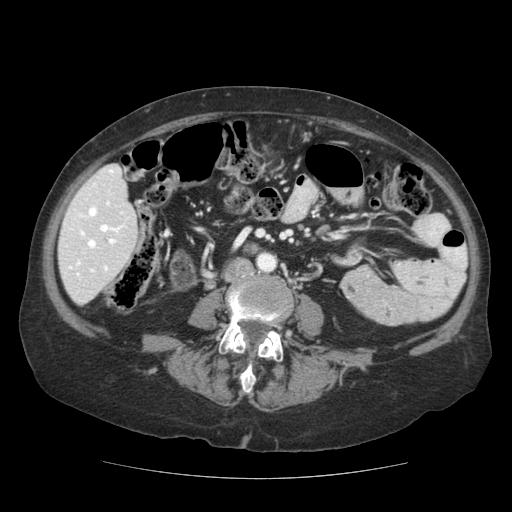
Contrast-enhanced abdominal CT (liver protocol), one axial slice. Position 37 of 111 along the scan axis. Reconstruction kernel STANDARD. 140 kVp. Soft-tissue window (W 400 / L 40 HU). 512 × 512 image matrix, field of view 360 × 360 mm. From the clinical record (not read from this slice): diagnosis: hepatocellular carcinoma (patient treated with transarterial chemoembolisation; whether this scan precedes or follows treatment is not stated here); TNM stage (as recorded): Stage-I; Child-Pugh class: A; tumour differentiation: moderately-poorly differentiated; tumour nodularity: uninodular.
Structures marked on this image (semi-automatic segmentation, software-assisted and operator-edited):
- liver parenchyma outside the tumour (the mass and vessels are separate outlines, so this box may not span the whole liver): box from (x=58, y=164) to (x=138, y=304) px
- liver vessels: (x=68, y=169)–(x=129, y=276)